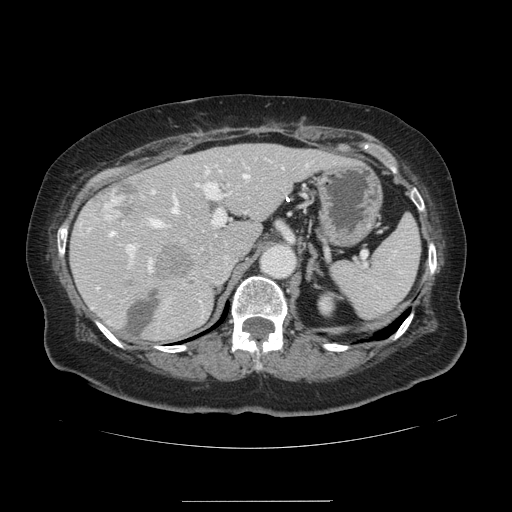
Contrast-enhanced abdominal CT, one axial slice. Position 85 of 141 along the scan axis. 120 kVp. Intravenous contrast given. Soft-tissue window (W 400 / L 40 HU). 2.5 mm slice thickness. 512 × 512 image matrix, field of view 393 × 393 mm. Female patient, age 74 years. From the clinical record (not read from this slice): diagnosis: colorectal cancer liver metastases, imaged before liver resection; multiple liver metastases: yes; largest metastasis: 7 cm; disease in both lobes: yes.
Outlined on this slice (manually delineated by an expert):
- hepatic veins: bounding box [x1, y1, x2, y2] px = [110, 174, 247, 235]
- liver: [72, 144, 339, 341]
- planned liver remnant (the part of the liver to remain after resection): [72, 144, 339, 340]
- portal vein (with intrahepatic branches): [126, 164, 307, 268]
- liver metastasis: [95, 179, 159, 225]
- liver metastasis: [126, 291, 160, 335]
- liver metastasis: [157, 245, 193, 278]